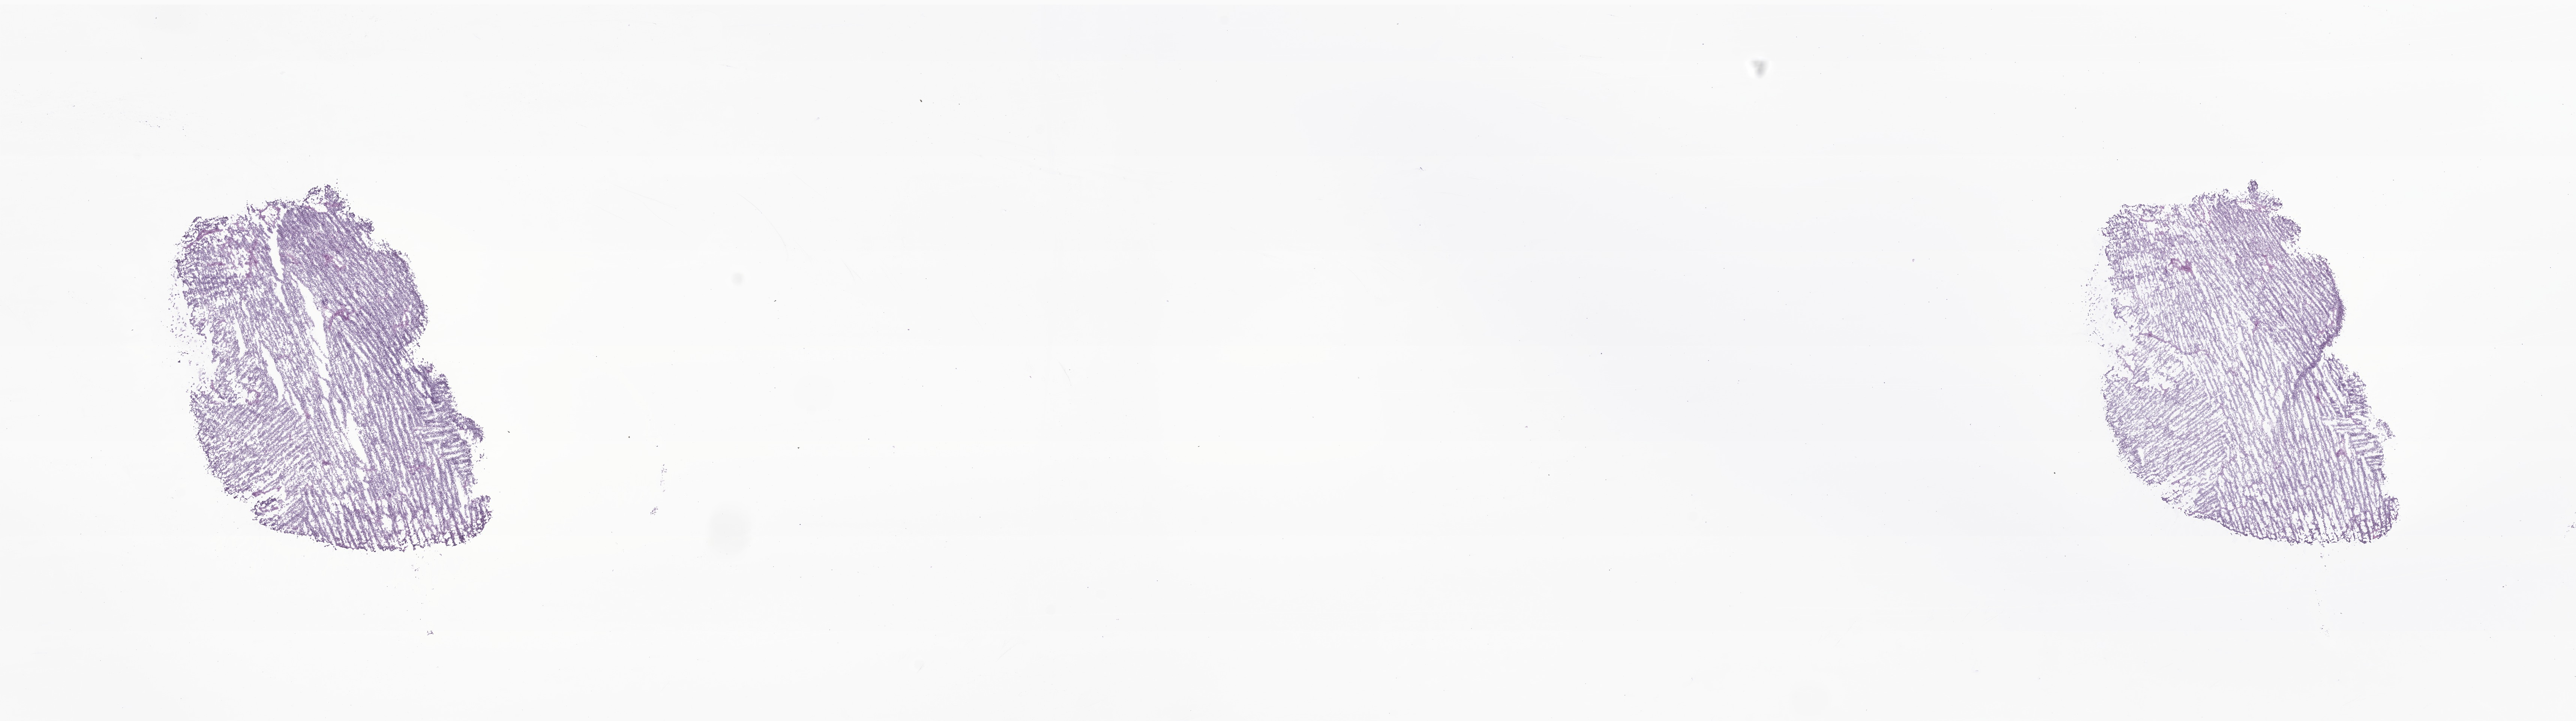
Haematoxylin and eosin whole-slide image of tumor tissue from the nasopharynx — low-resolution overview of the scanned area, about 29.0 x 8.1 mm, frozen section. Patient: male, age 49 months (4 years 1 month).
Diagnosis (ICD-O-3 morphology term): Embryonal rhabdomyosarcoma, NOS.